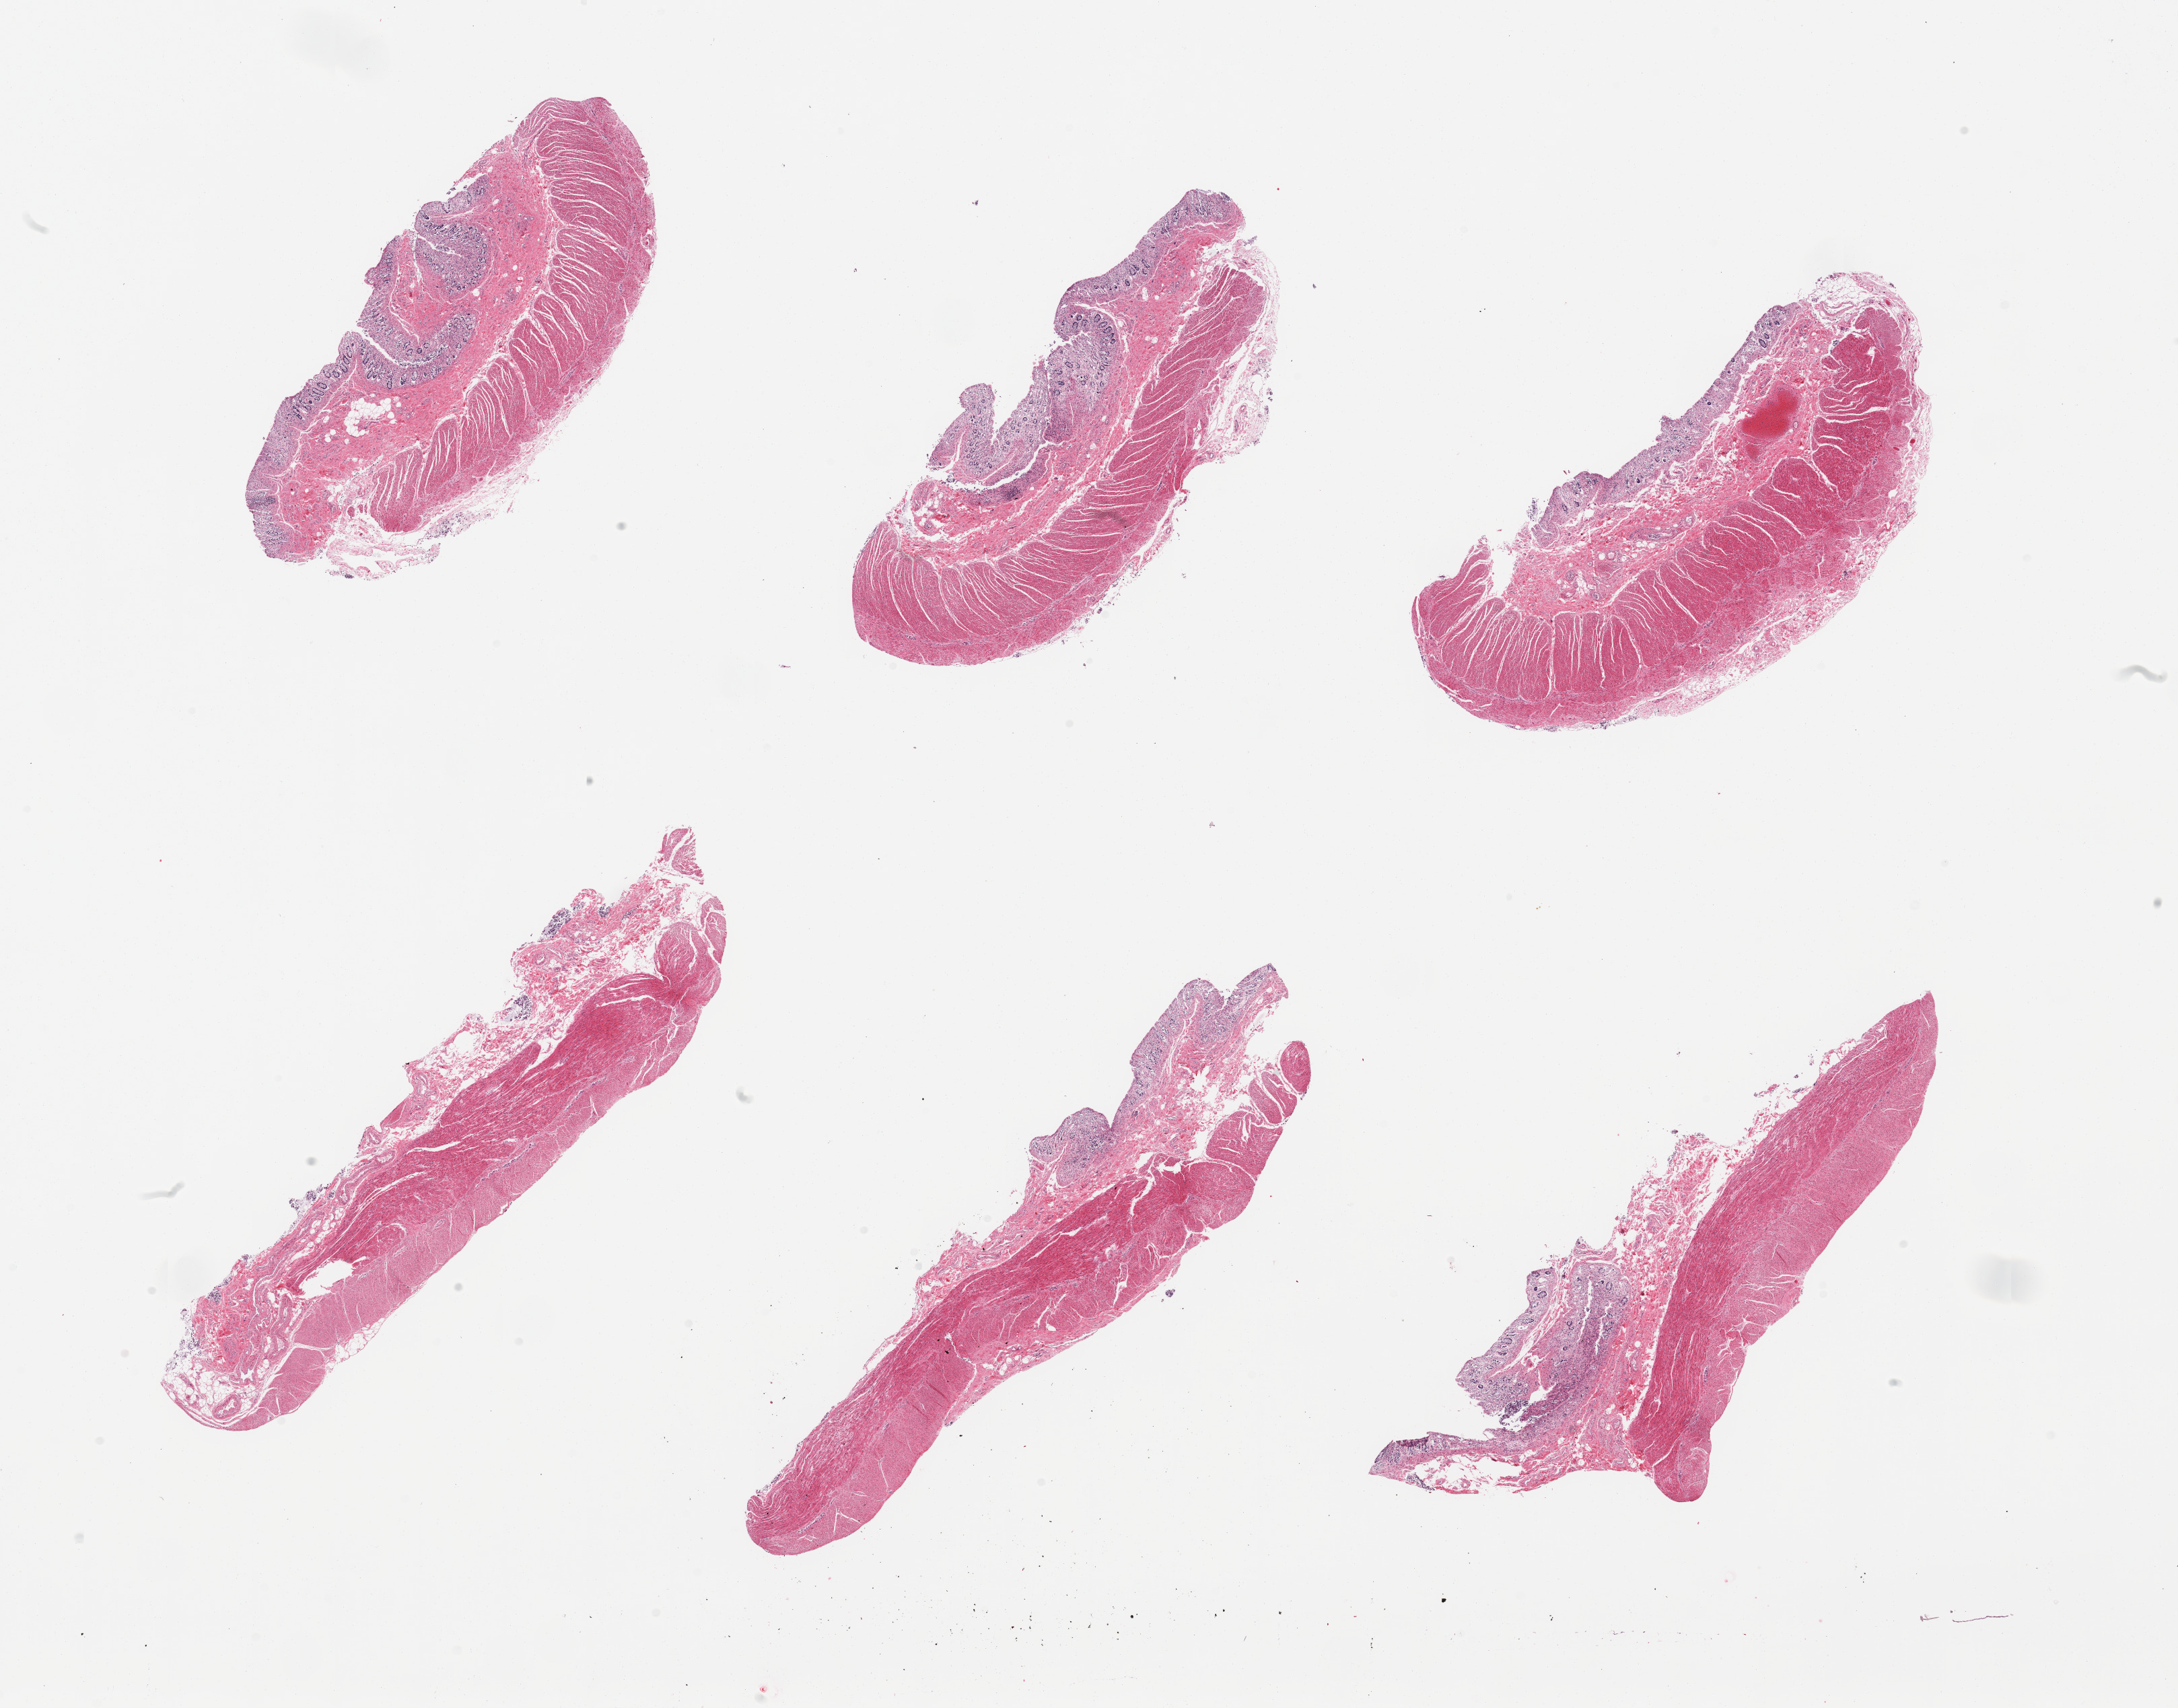
Digitized hematoxylin and eosin (H&E)-stained section, a low-resolution overview of the entire scanned area, about 25.6 x 20.1 mm (acquisition: 20x scan); PAXgene-fixed, paraffin-embedded tissue; sampled site (target tissue): transverse colon; tissue donor sample. Donor: female.
Pathologist's review note for this sample: 6 pieces; mucosa largely autolyzed, muscularis moderately autolyzed.